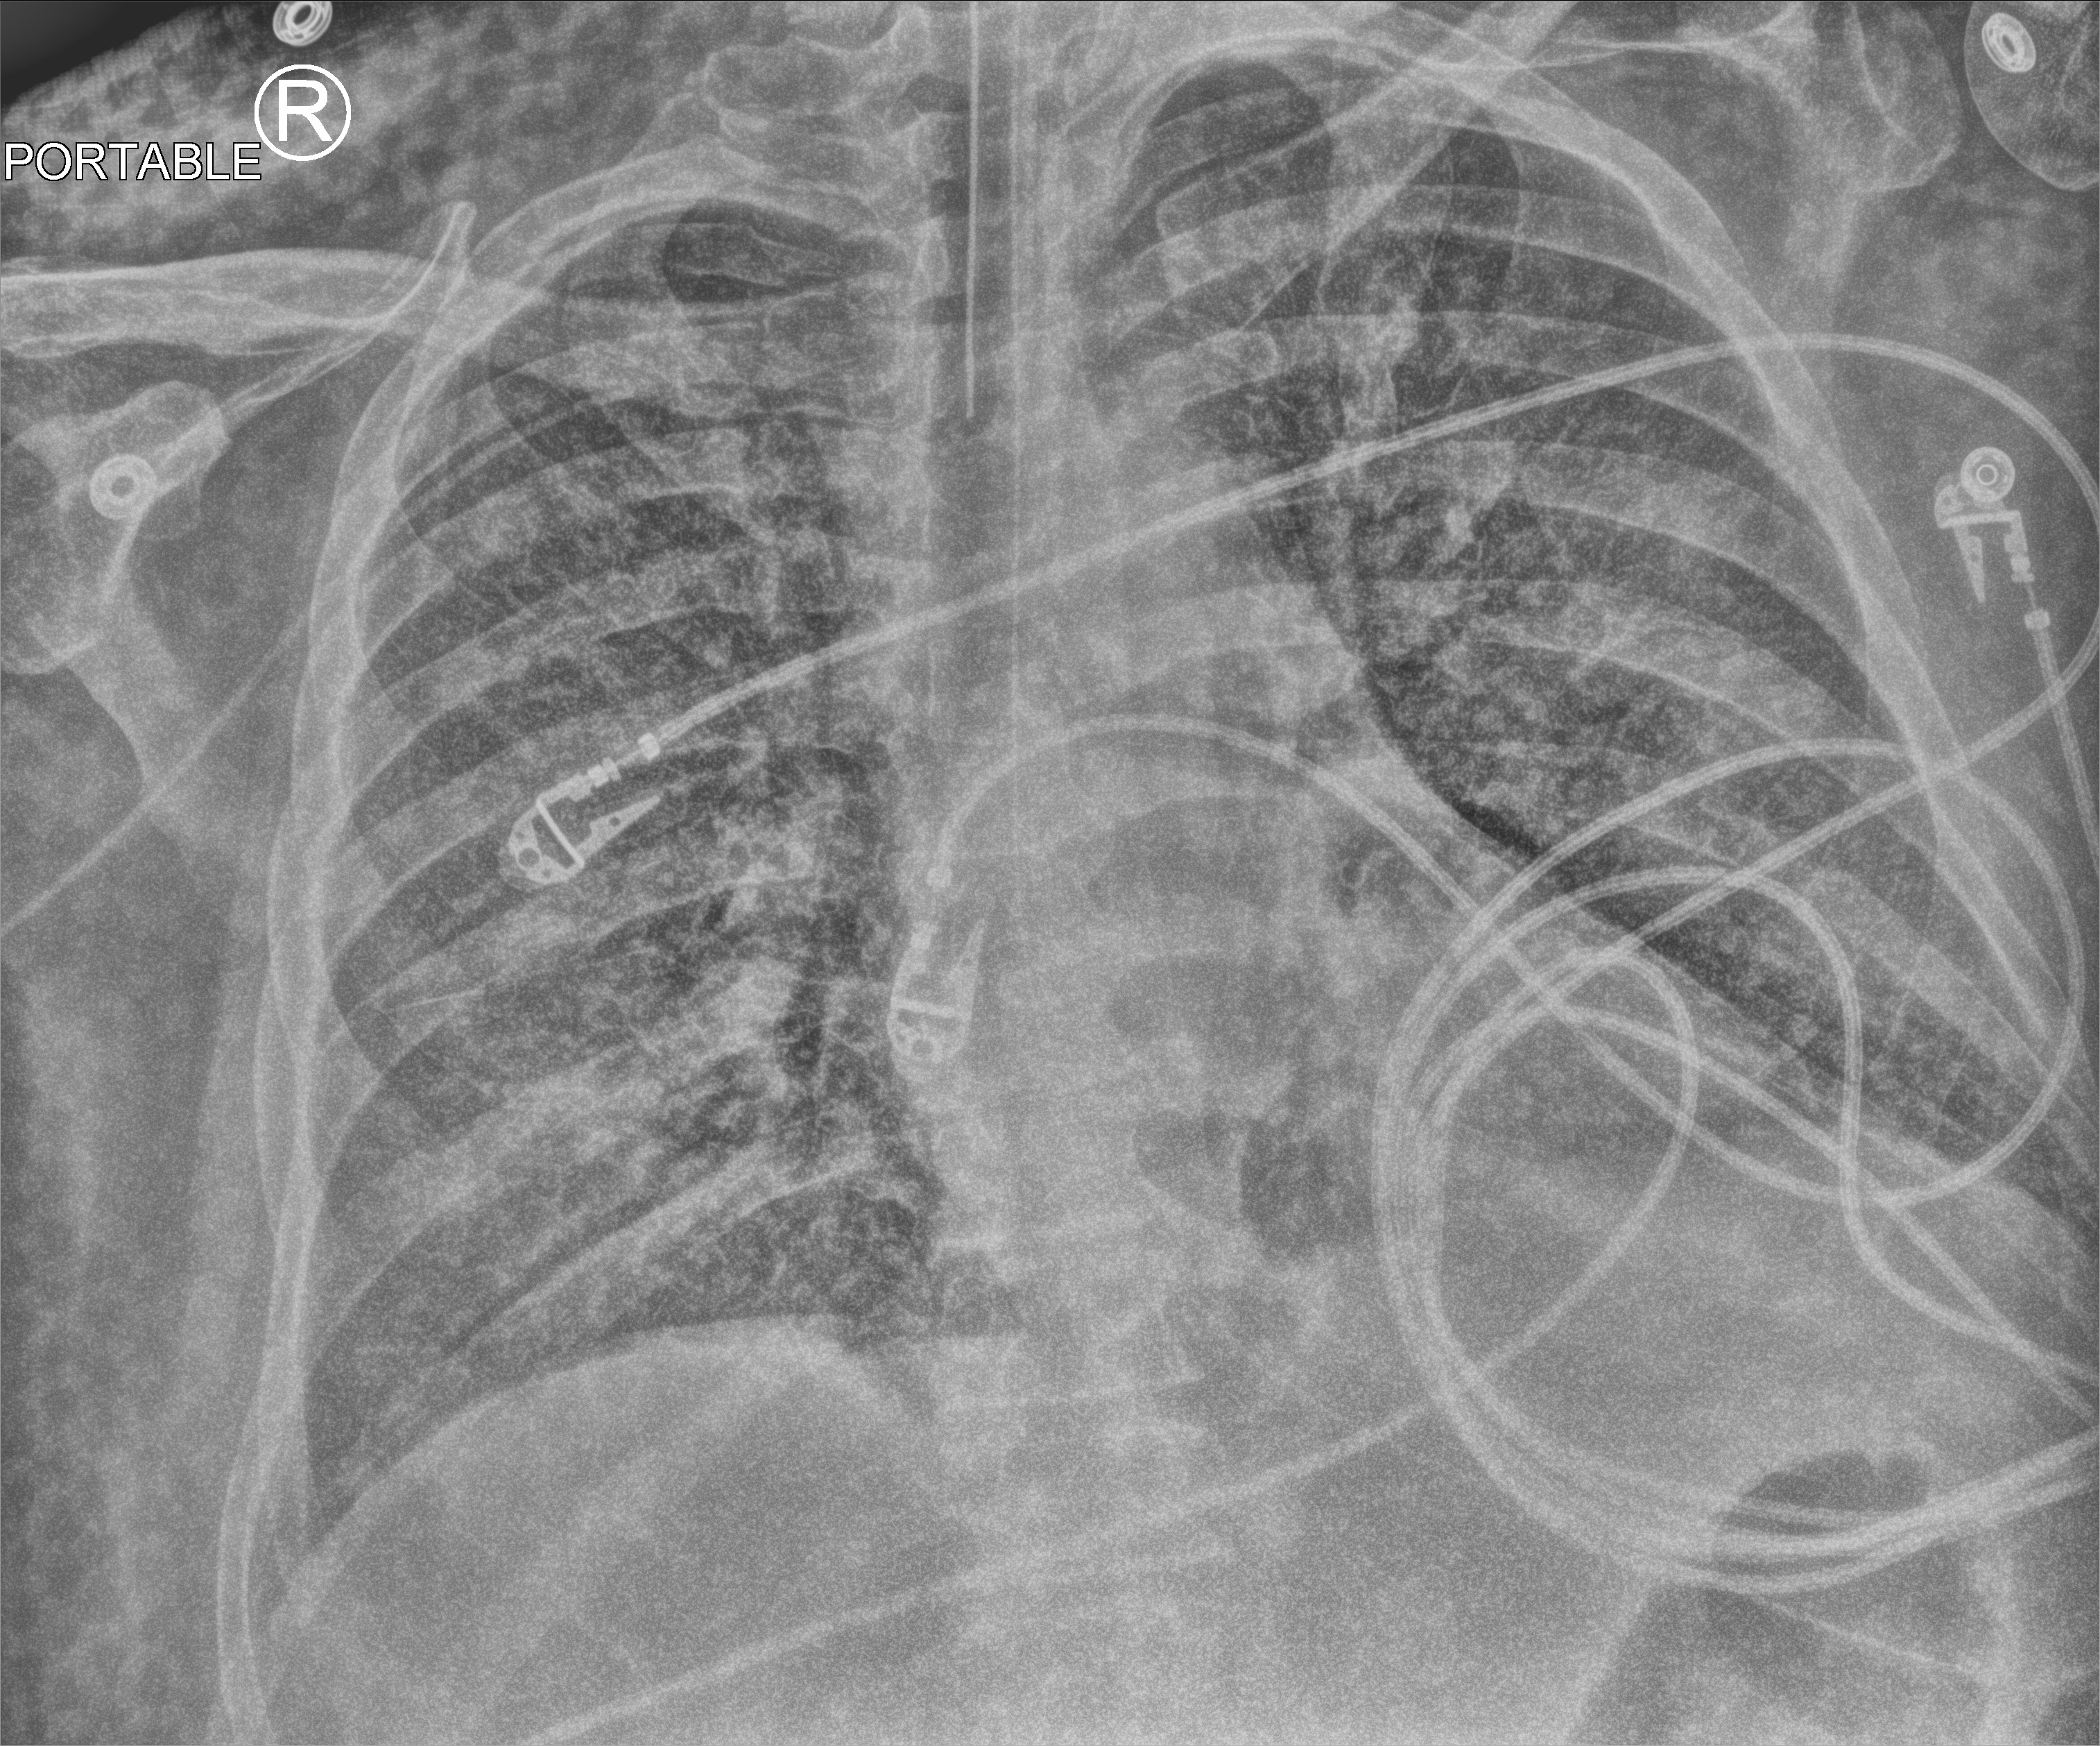
Chest X-ray (portable); anteroposterior (AP) projection. Adult patient hospitalised with COVID-19, age 18–59 years.
From the hospital-stay record, not from the radiograph (when in the stay this image was taken is not recorded):
- mechanically ventilated during this hospital stay: yes